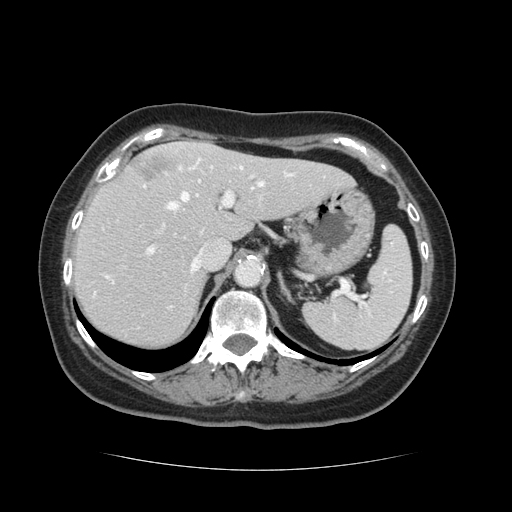
Contrast-enhanced abdominal CT, one axial slice. Position 89 of 128 along the scan axis. 120 kVp. Intravenous contrast given. Soft-tissue window (W 400 / L 40 HU). 2.5 mm slice thickness. 512 × 512 image matrix, field of view 366 × 366 mm. Female patient, age 67 years. From the clinical record (not read from this slice): diagnosis: colorectal cancer liver metastases, imaged before liver resection; multiple liver metastases: yes; largest metastasis: 3 cm; chemotherapy before resection: no.
Annotated regions visible in this slice (expert manual segmentation):
- hepatic veins: bounding box [x1, y1, x2, y2] px = [168, 167, 293, 271]
- liver: [73, 144, 351, 349]
- planned liver remnant (the part of the liver to remain after resection): [73, 157, 351, 349]
- portal vein (with intrahepatic branches): [149, 165, 255, 253]
- liver metastasis: [136, 157, 175, 182]